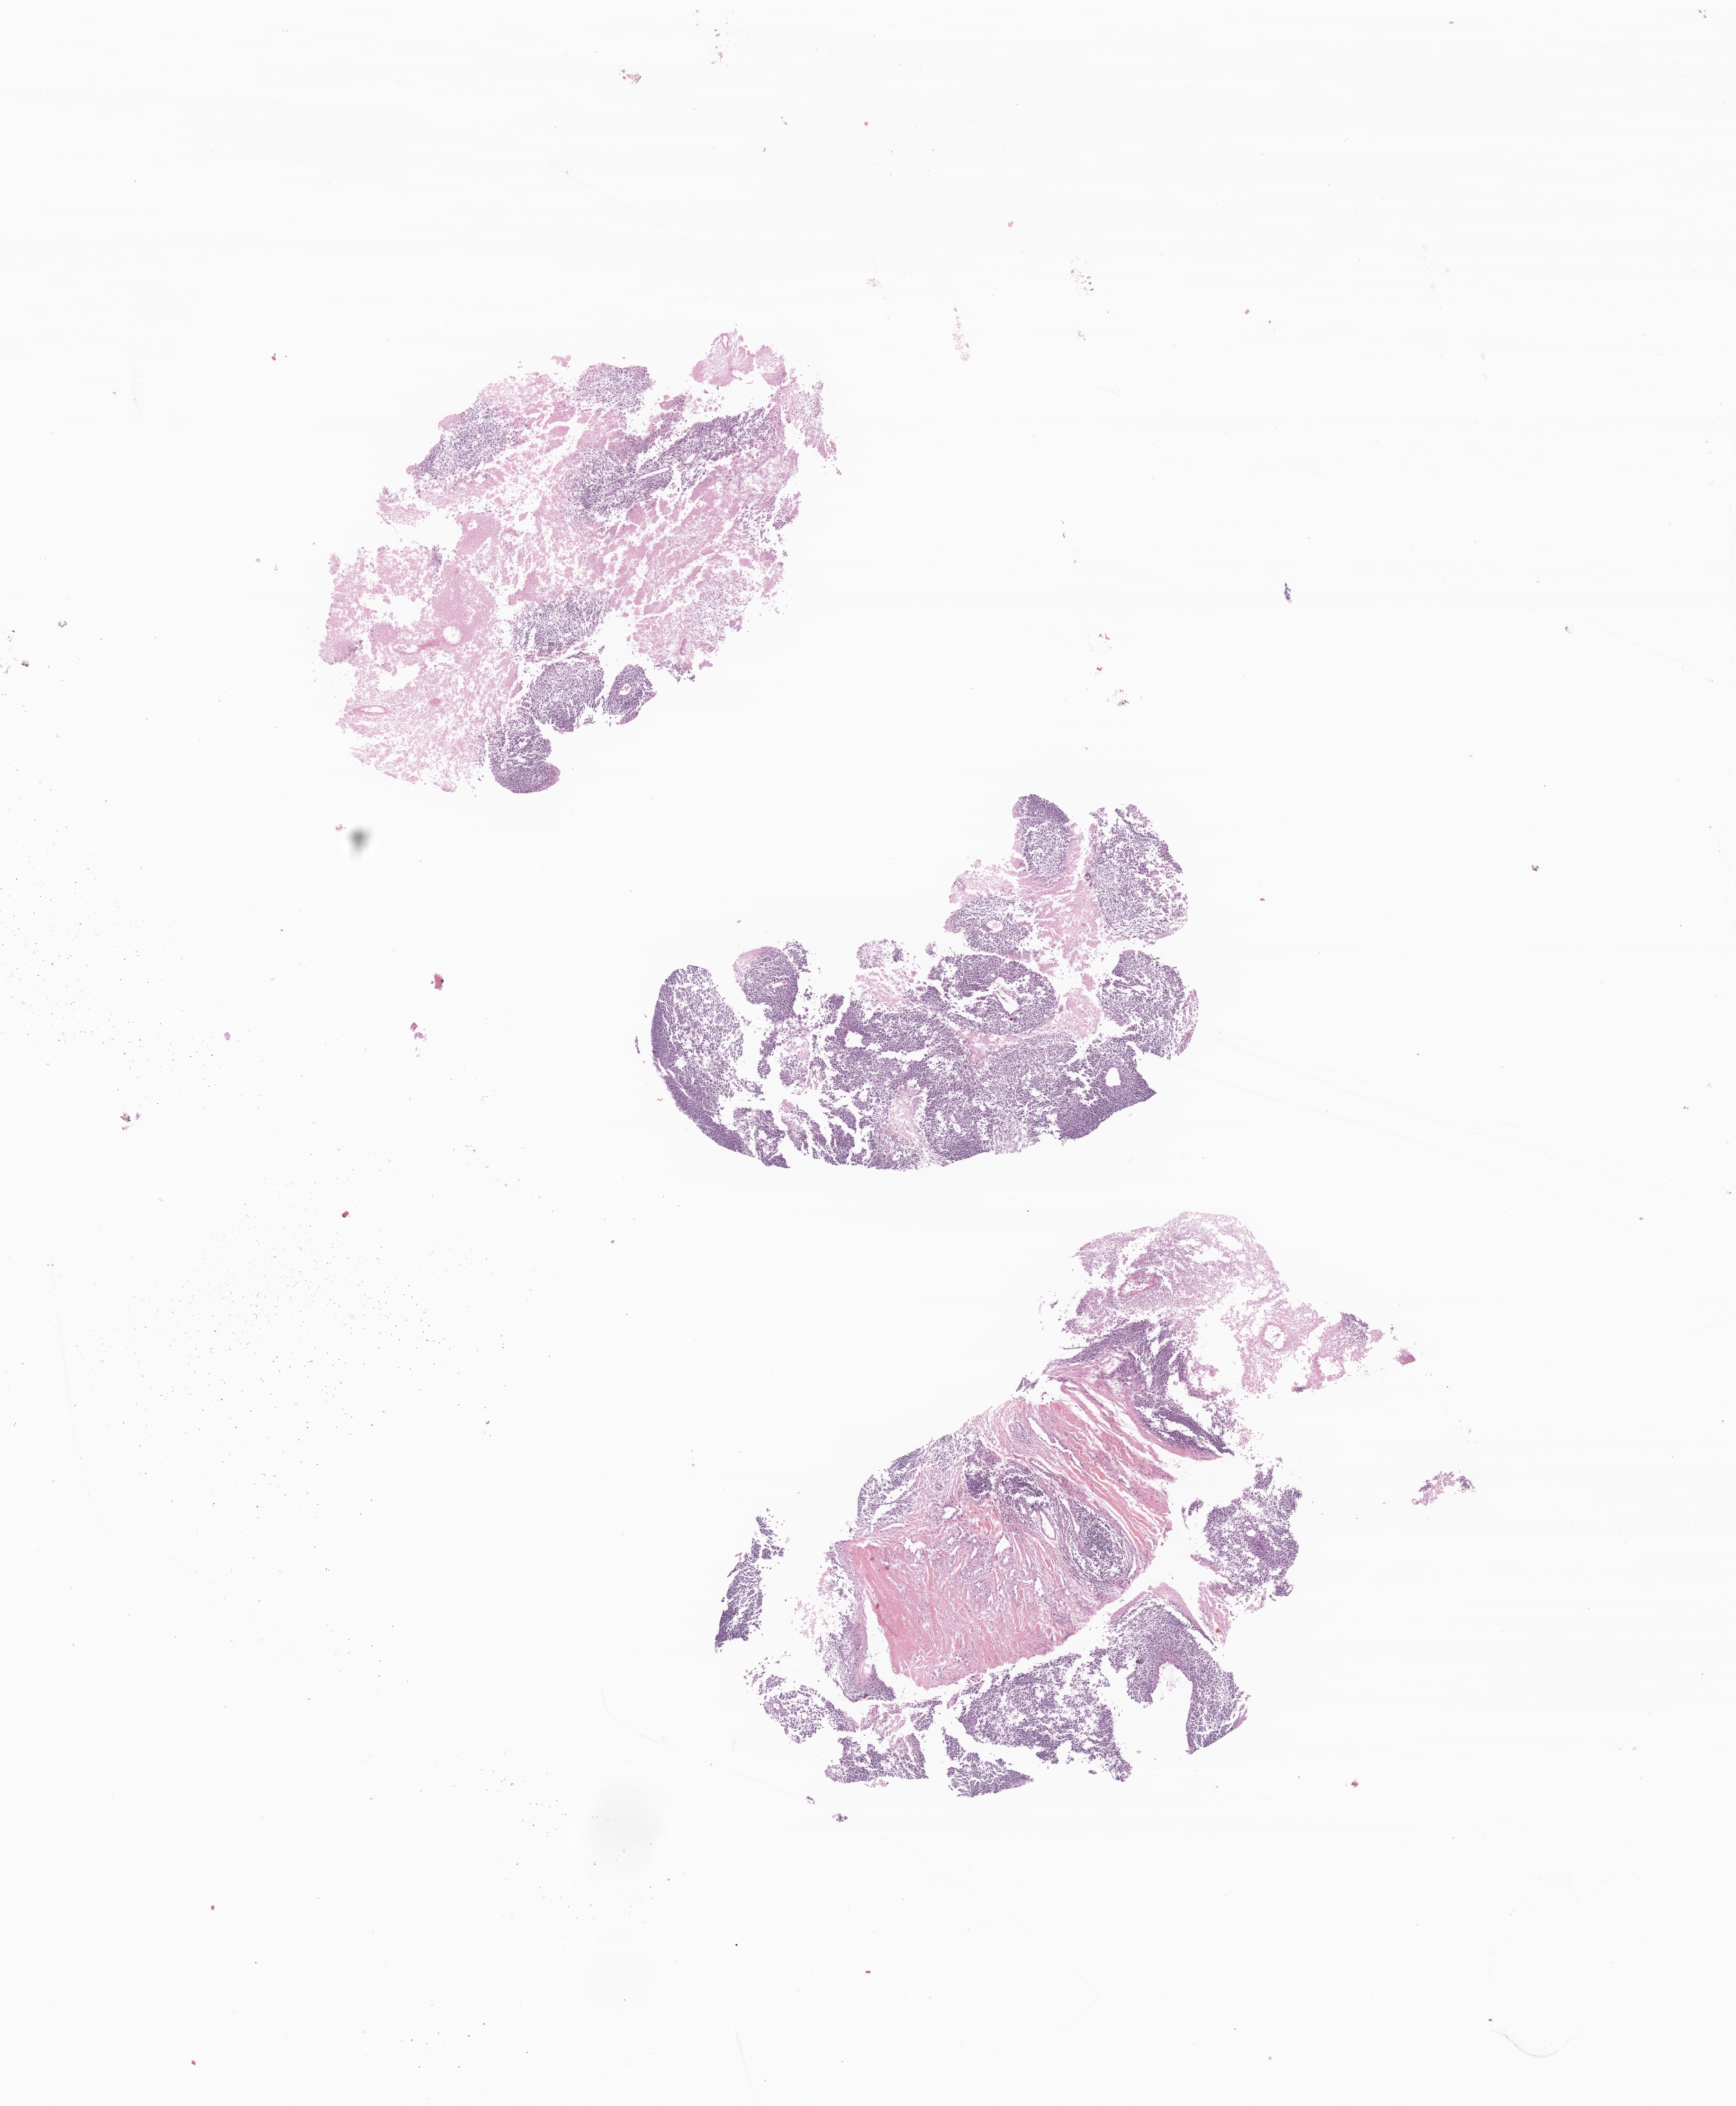
Digitized hematoxylin and eosin (H&E)-stained section of tumor tissue from the skin of trunk — shown as a low-resolution overview of the whole scanned area (about 10.6 x 12.8 mm), FFPE section. Patient: male, age 145 months.
Recorded diagnosis: Sarcoma, NOS.